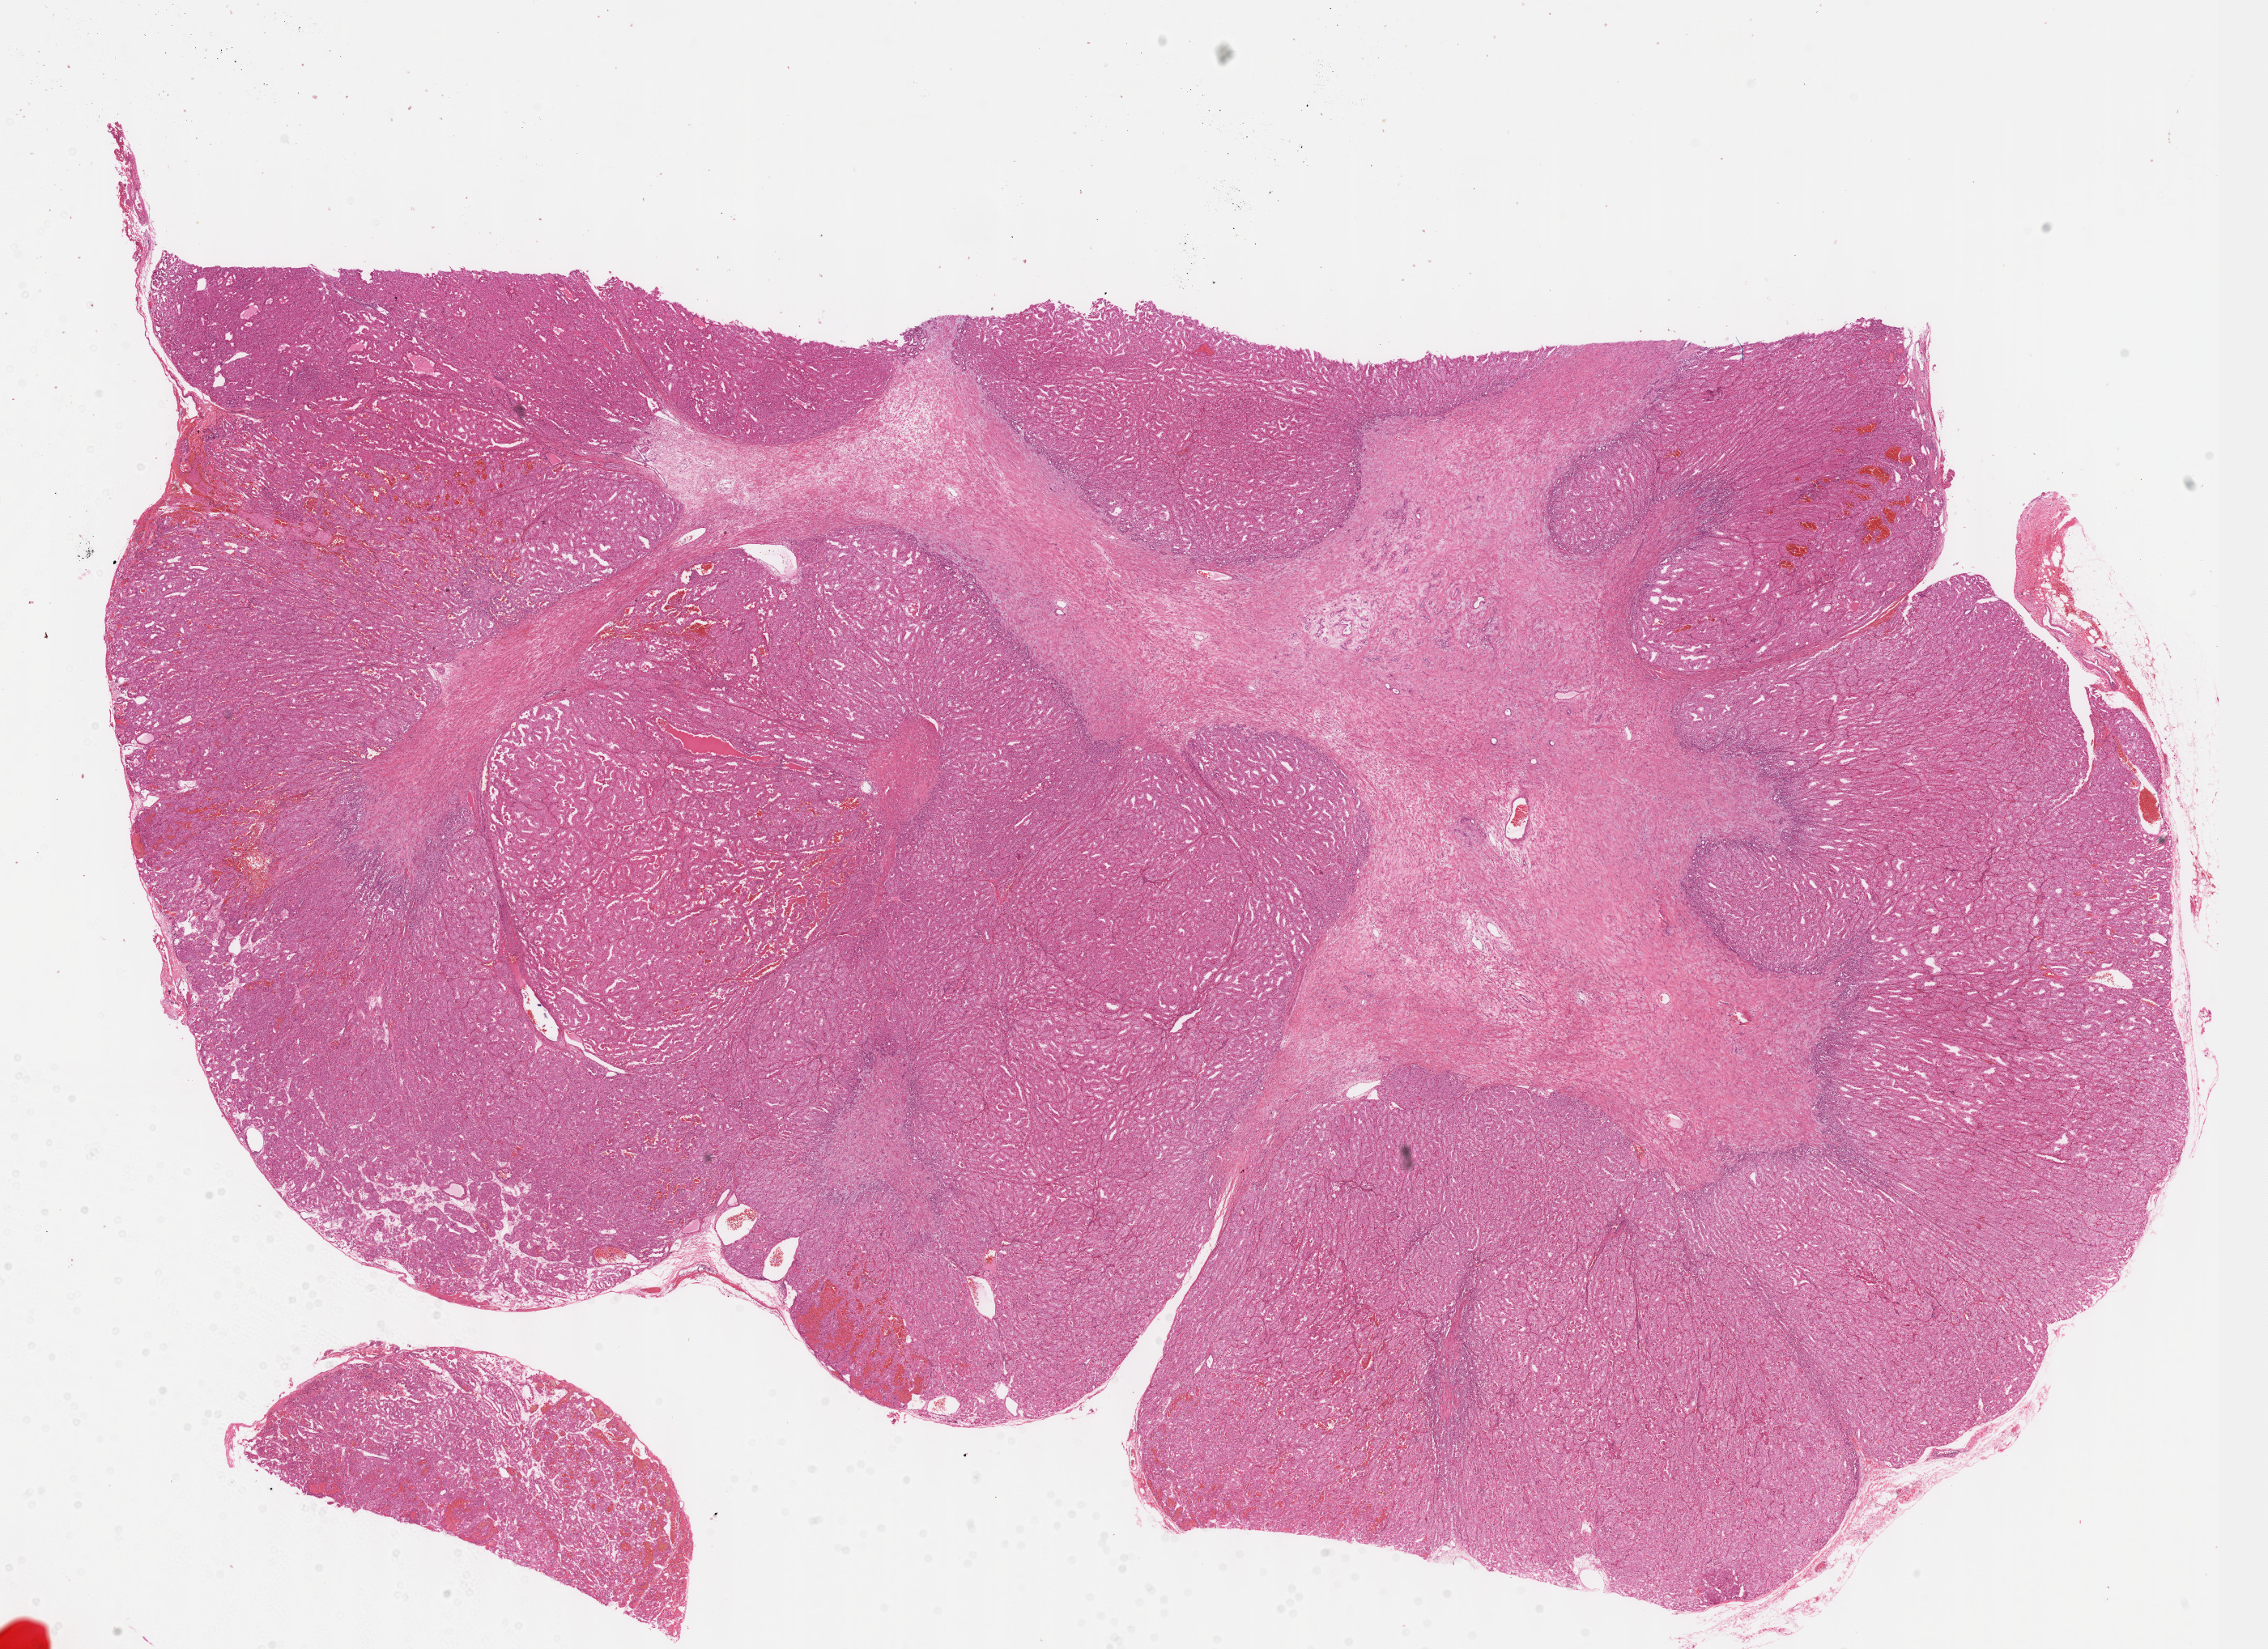
Hematoxylin and eosin (H&E) stained whole-slide image, shown as a low-resolution overview of the whole scanned area (about 22.6 x 16.5 mm, acquisition: 40x scan), FFPE section, primary tumour sample from the kidney. Male patient; age at initial diagnosis 53 years. Composition of this section per pathologist review: tumour cells 65%, tumour nuclei 95%, normal cells 0%, stromal cells 35%, necrosis 0%. Infiltration values recorded for this section: lymphocyte infiltration 2%, monocyte infiltration 0%, neutrophil infiltration 1%.
TNM: T1b NX. Laterality: left. Histologic diagnosis: Renal cell carcinoma, chromophobe type. AJCC pathologic stage: I (7th edition).